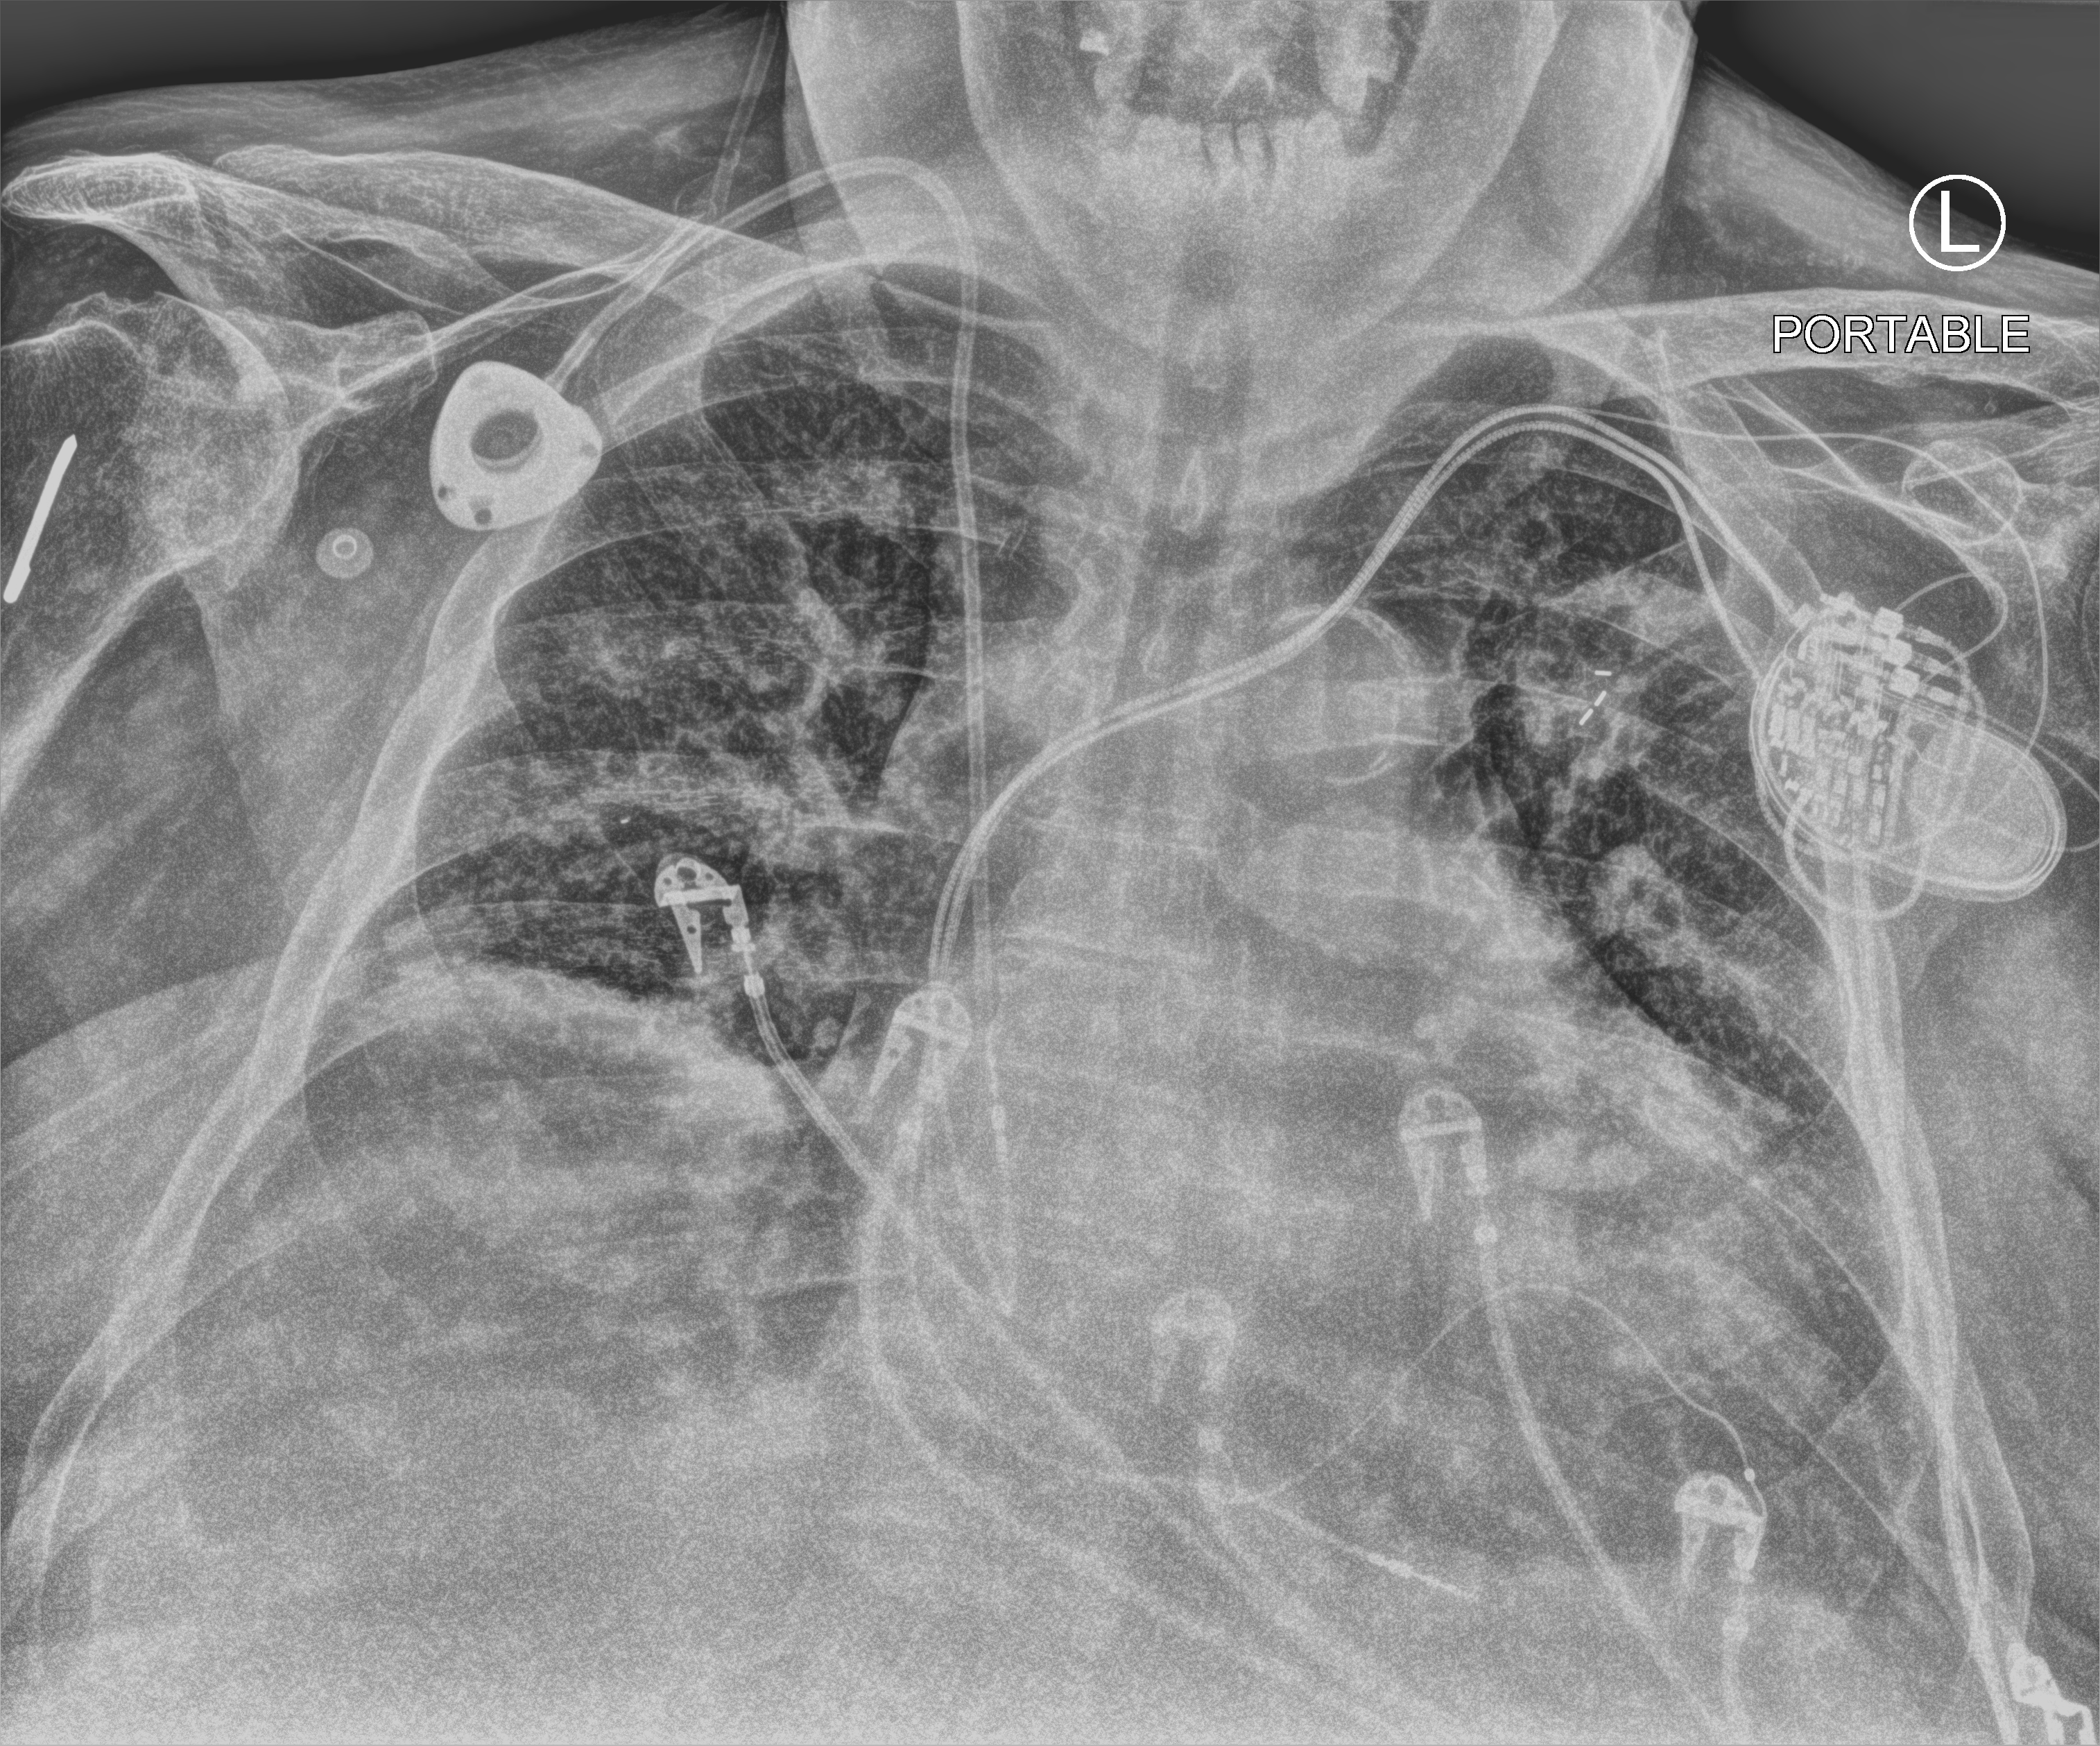
Bedside chest radiograph (computed radiography), anteroposterior (AP) projection. Patient hospitalised with COVID-19; male, aged 60–74 years.
Hospital-stay facts (about this admission, not read from this image; timing relative to this image not recorded):
- admitted to intensive care during this hospital stay: yes
- mechanically ventilated during this hospital stay: no